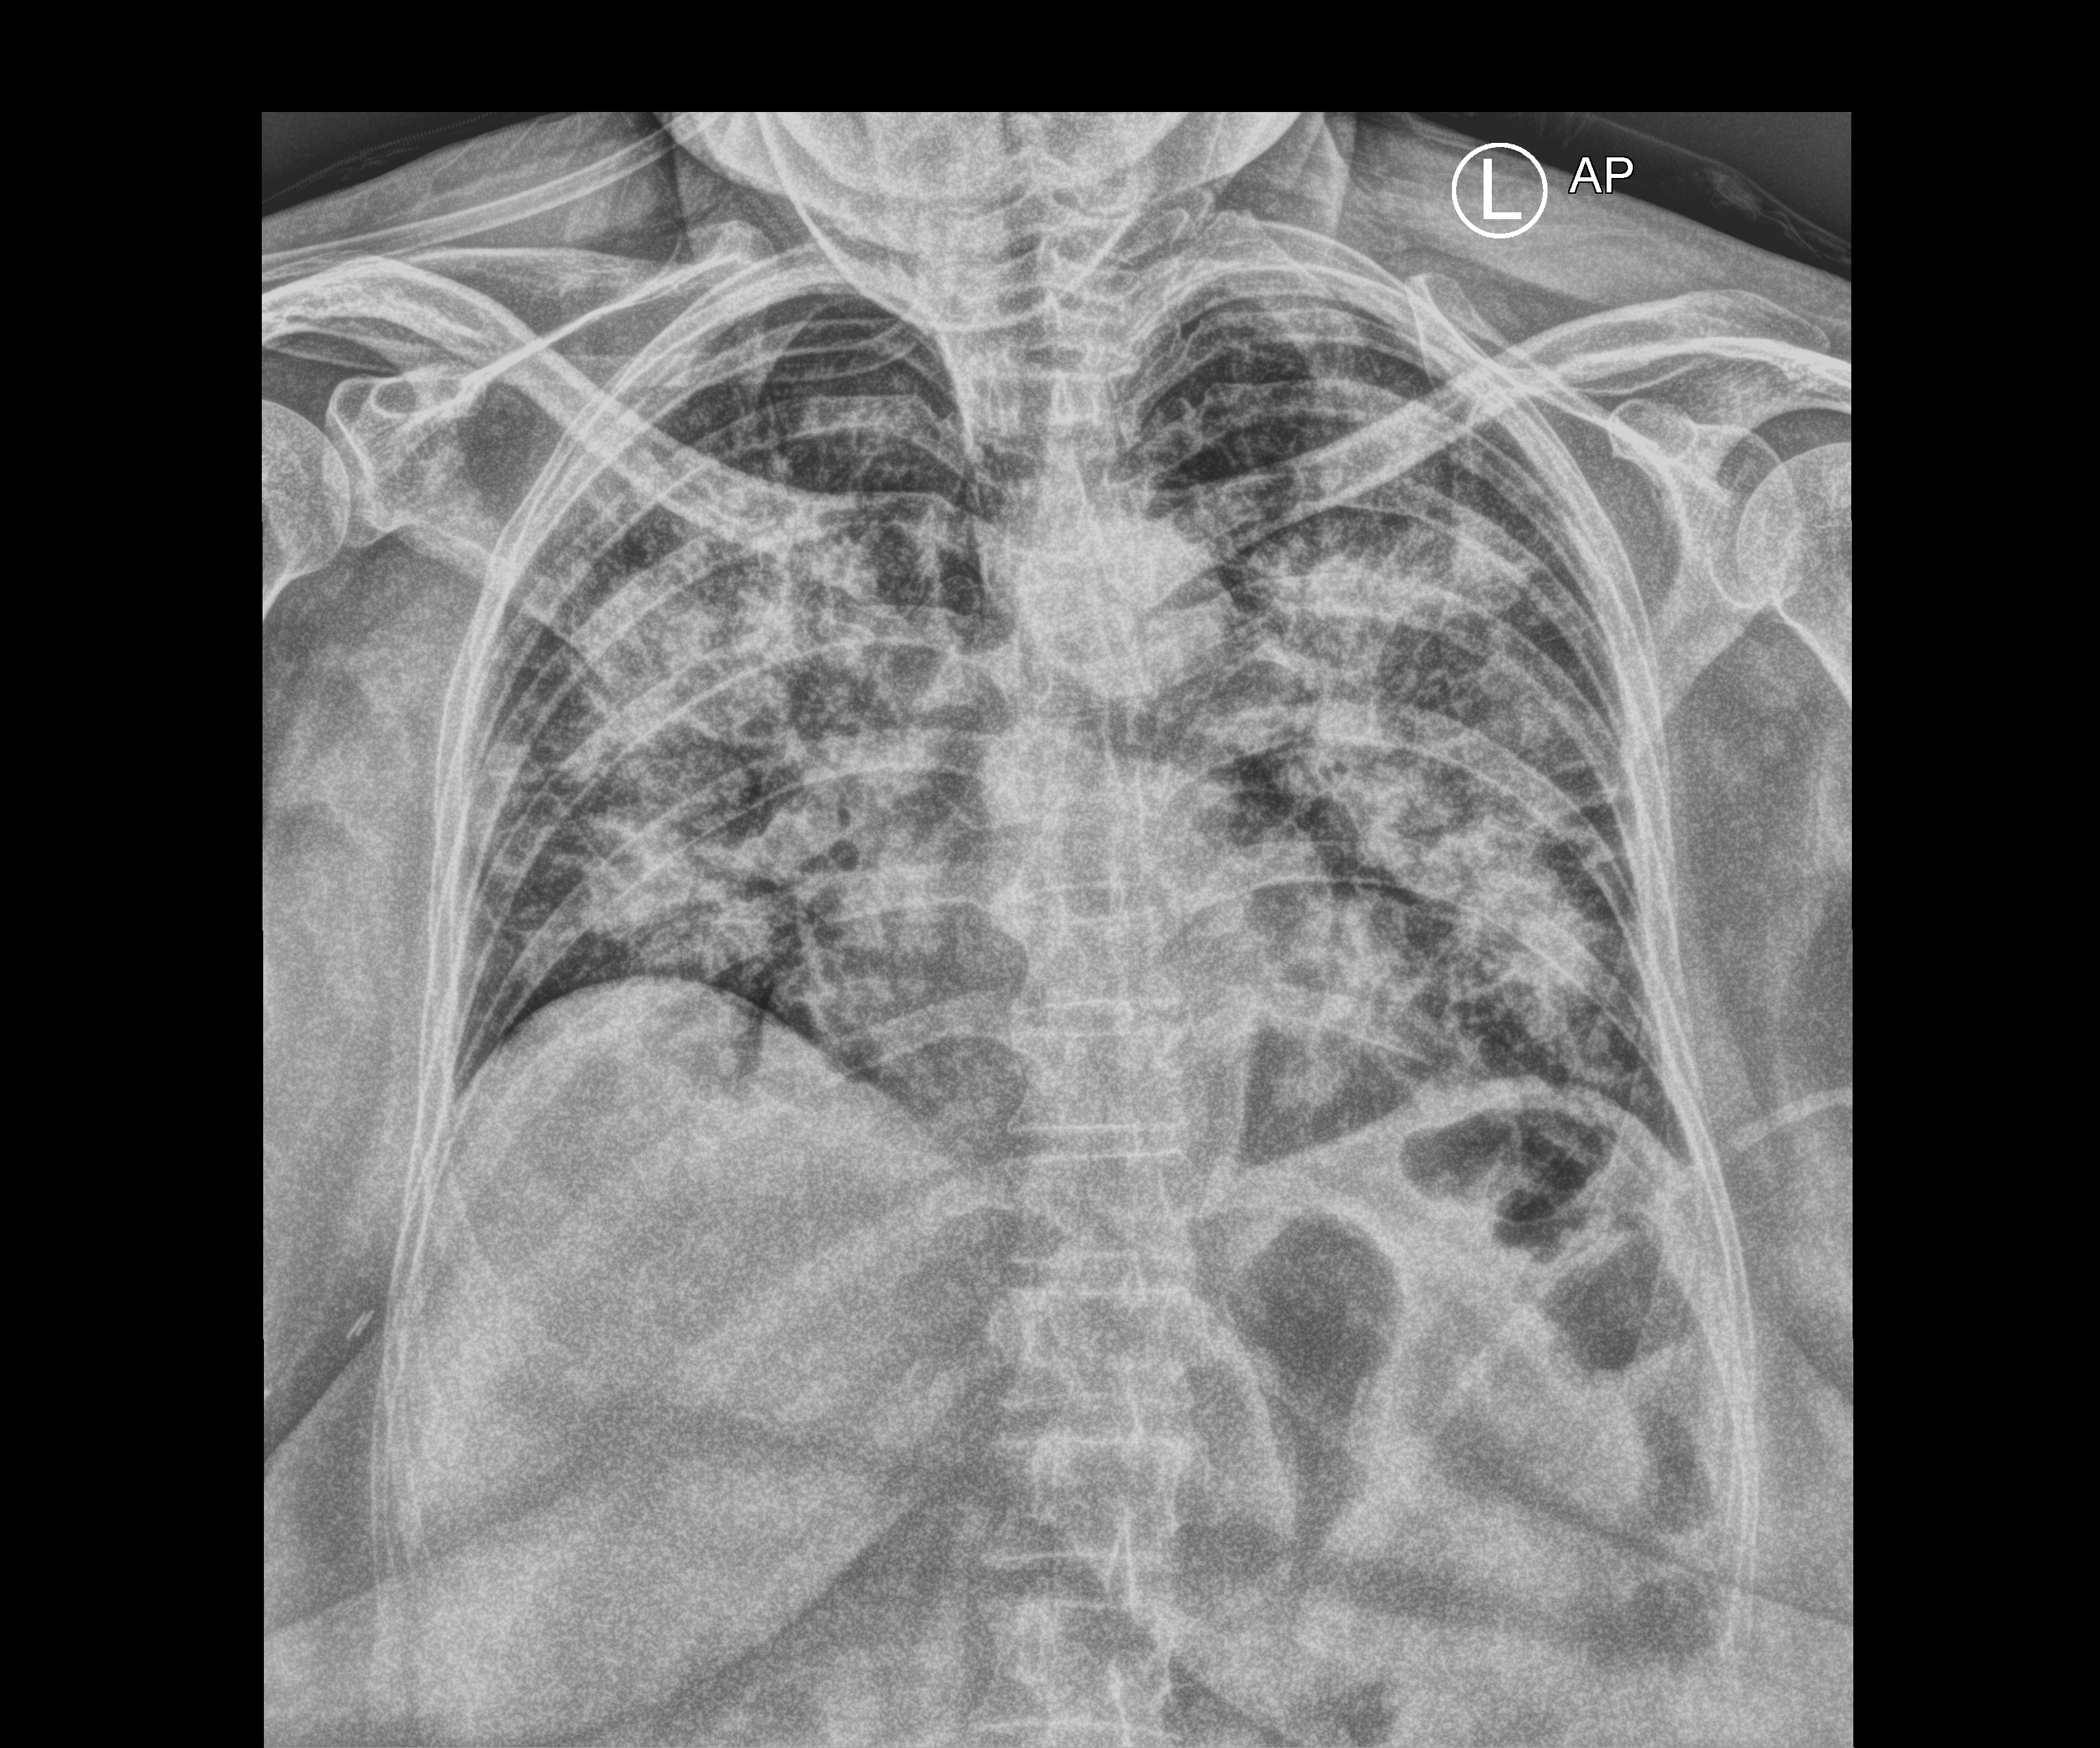
Portable chest radiograph; anteroposterior (AP) projection. Female patient hospitalised with COVID-19, age 60–74 years.
From the hospital-stay record, not from the radiograph (when in the stay this image was taken is not recorded): mechanically ventilated during this hospital stay: no.